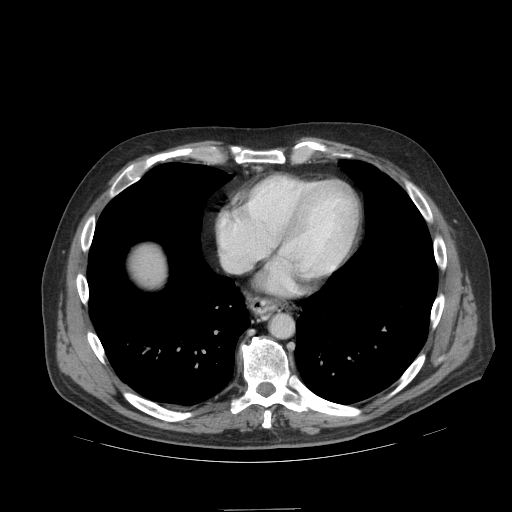
Contrast-enhanced abdominal CT (liver protocol), one axial slice; position 97 of 99 along the scan axis; soft-tissue window (W 400 / L 40 HU); 2.5 mm slice thickness; 512 × 512 image matrix, field of view 440 × 440 mm. From the clinical record (not read from this slice): diagnosis: hepatocellular carcinoma (patient treated with transarterial chemoembolisation; whether this scan precedes or follows treatment is not stated here); TNM stage (as recorded): Stage-I; Child-Pugh class: A; tumour differentiation: no biopsy; tumour nodularity: uninodular.
Outlined on this slice (semi-automatically segmented with operator editing):
- abdominal aorta: bounding box [x1, y1, x2, y2] px = [271, 315, 293, 337]
- liver parenchyma outside the tumour (the mass and vessels are separate outlines, so this box may not span the whole liver): [132, 246, 164, 284]